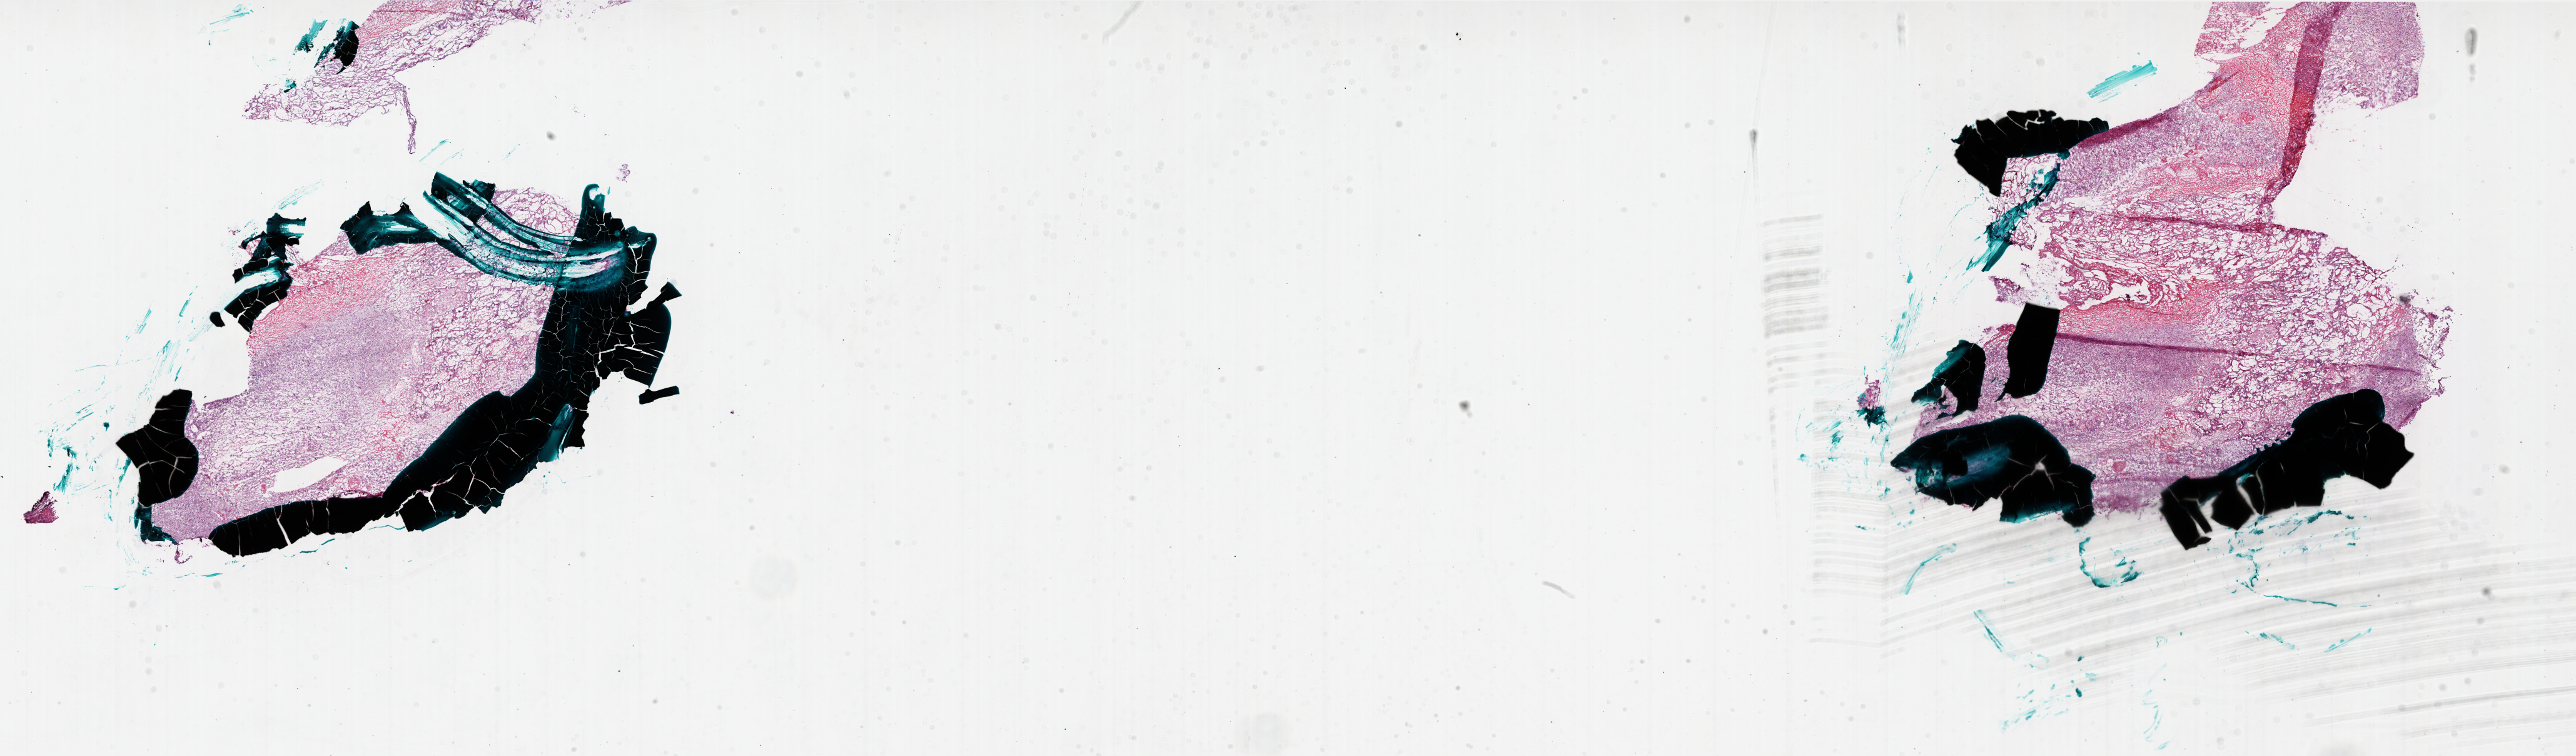
Whole-slide histology image, H&E — a low-resolution overview of the entire scanned area, about 33.0 x 9.7 mm (acquisition: 20x scan). Frozen section from the bottom of the tissue portion. Sample: primary tumour, brain. Female, age 51 years at initial diagnosis. Composition of this section per pathologist review: tumour cells 60%, tumour nuclei 100%, normal cells 0%, stromal cells 0%, necrosis 40%. Inflammatory infiltration, as recorded: lymphocyte infiltration 0%, monocyte infiltration 0%, neutrophil infiltration 0%.
* pathologic diagnosis: Glioblastoma